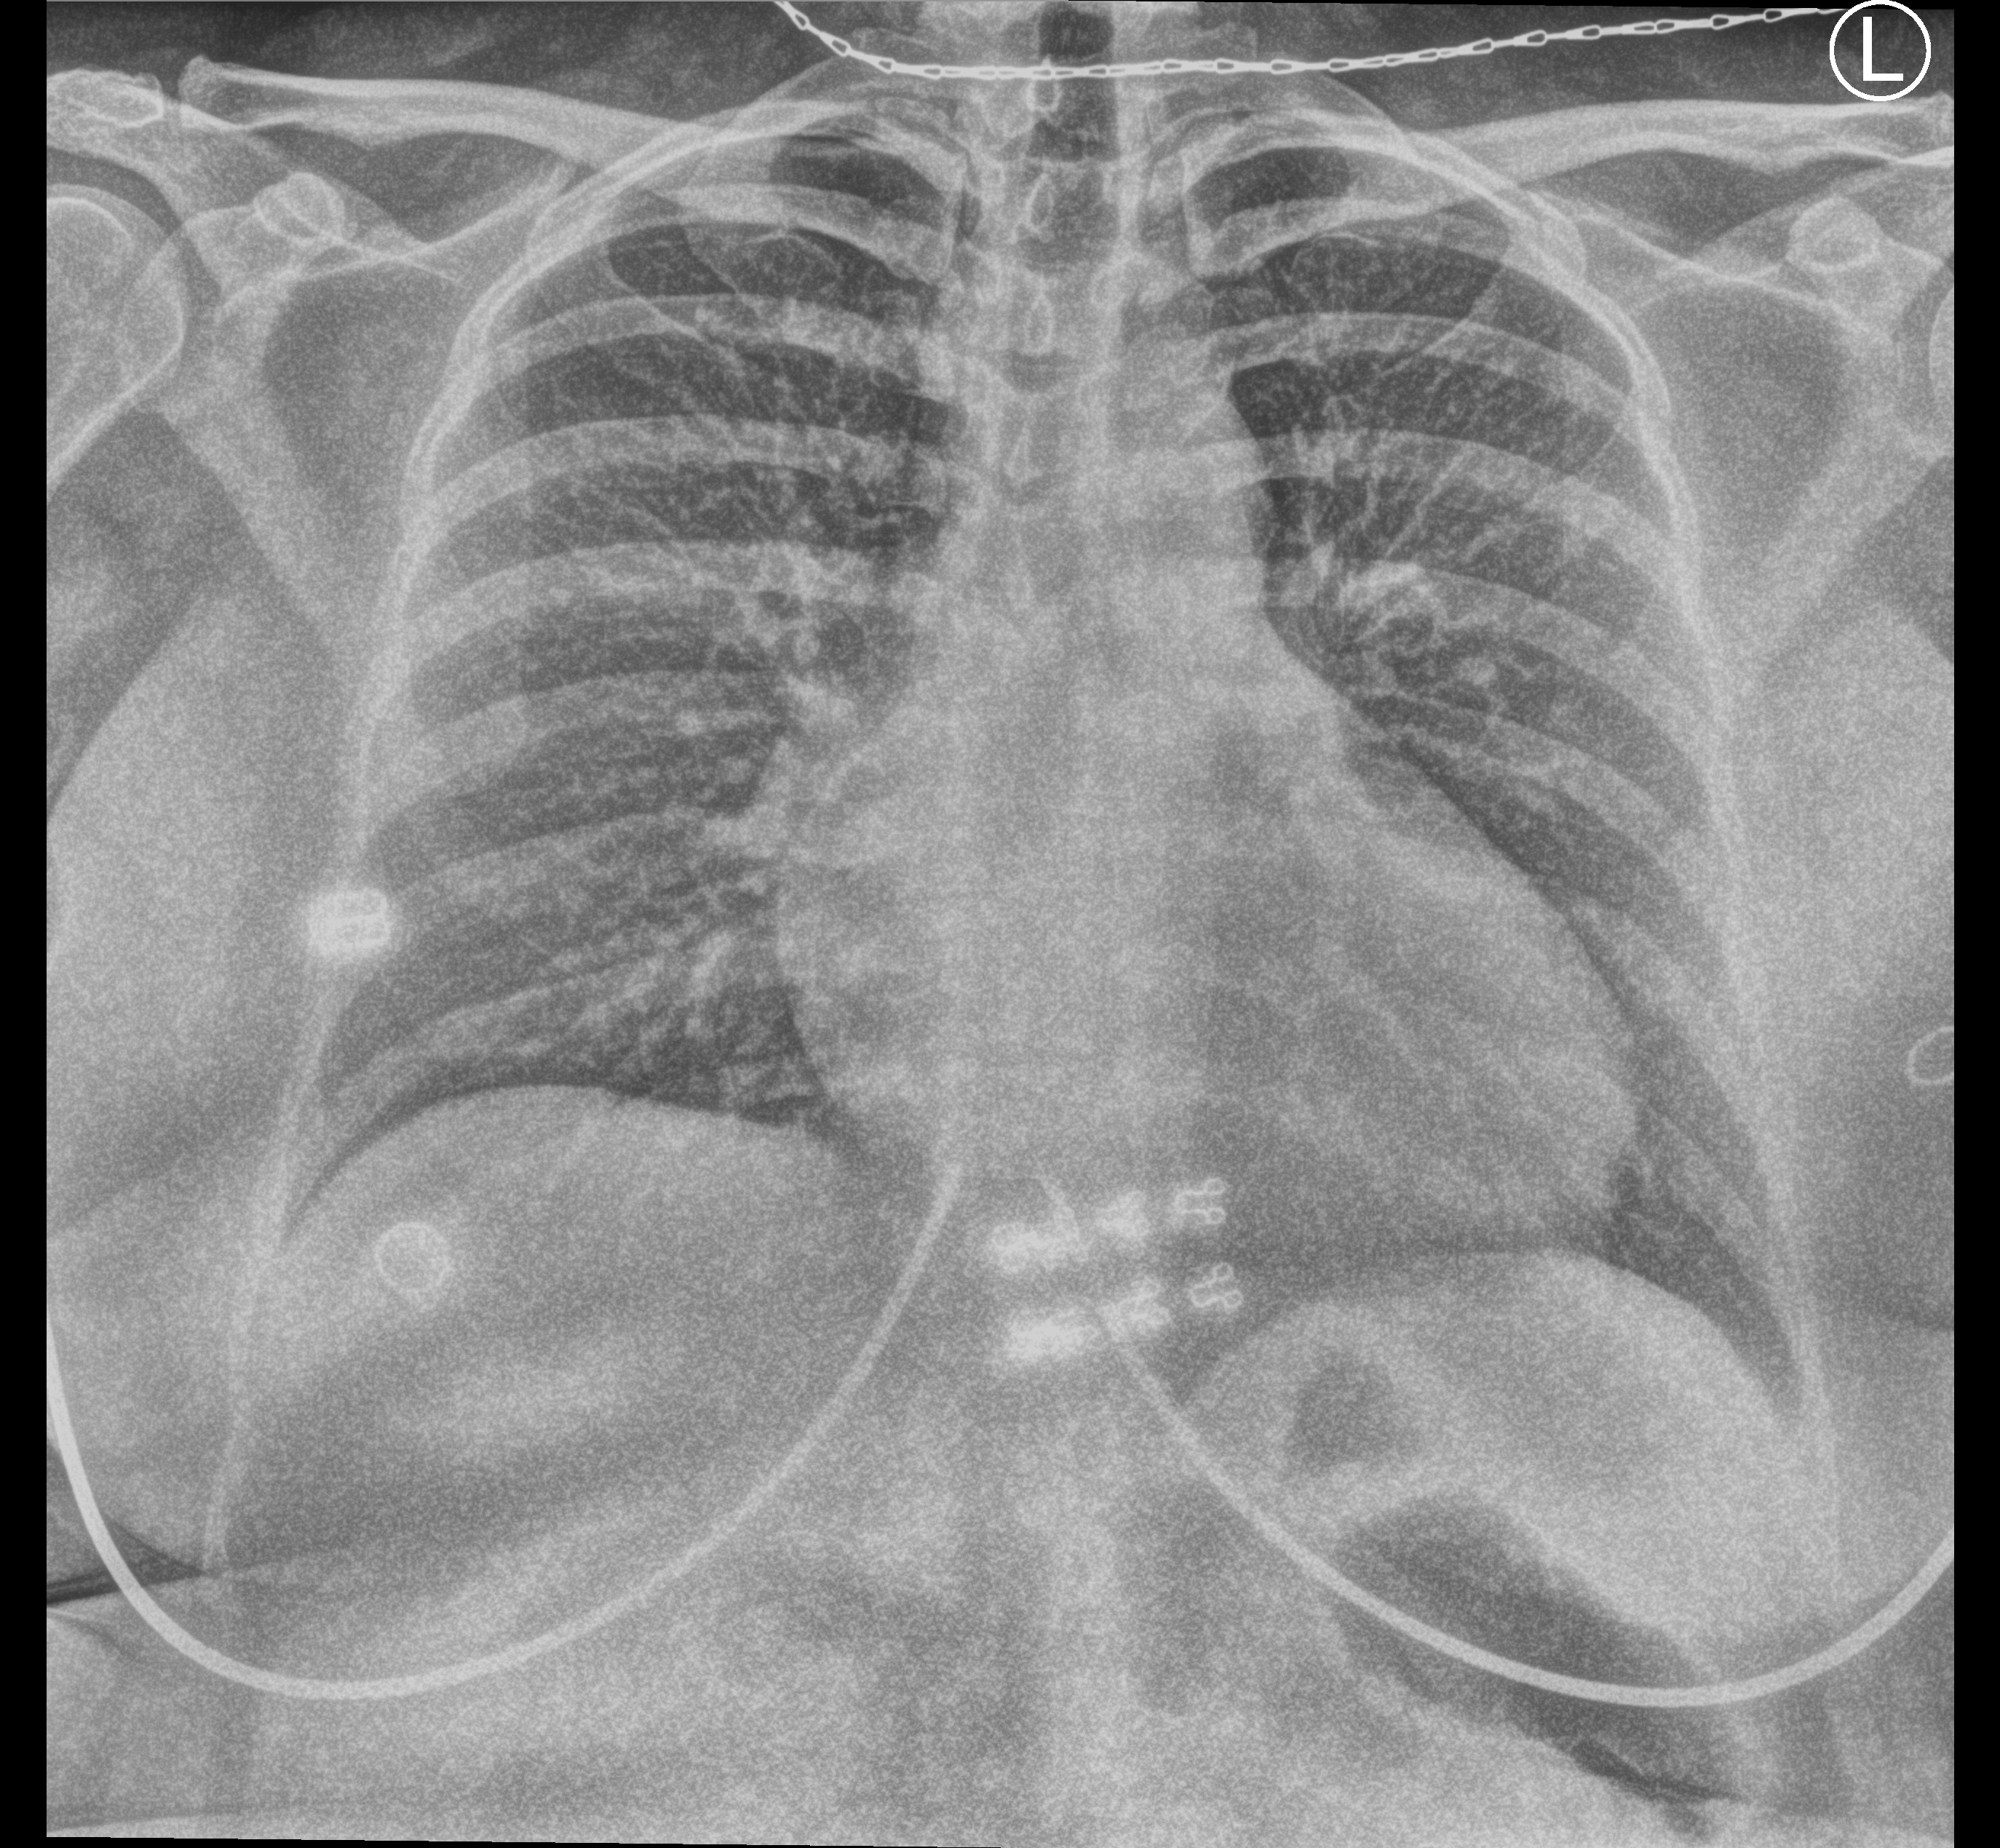
Portable chest radiograph, anteroposterior (AP) projection. Female patient hospitalised with COVID-19, age 18–59 years.
Admission-level facts for this patient (not findings on this image; timing relative to this image not recorded): admitted to intensive care during this hospital stay: no; mechanically ventilated during this hospital stay: no.